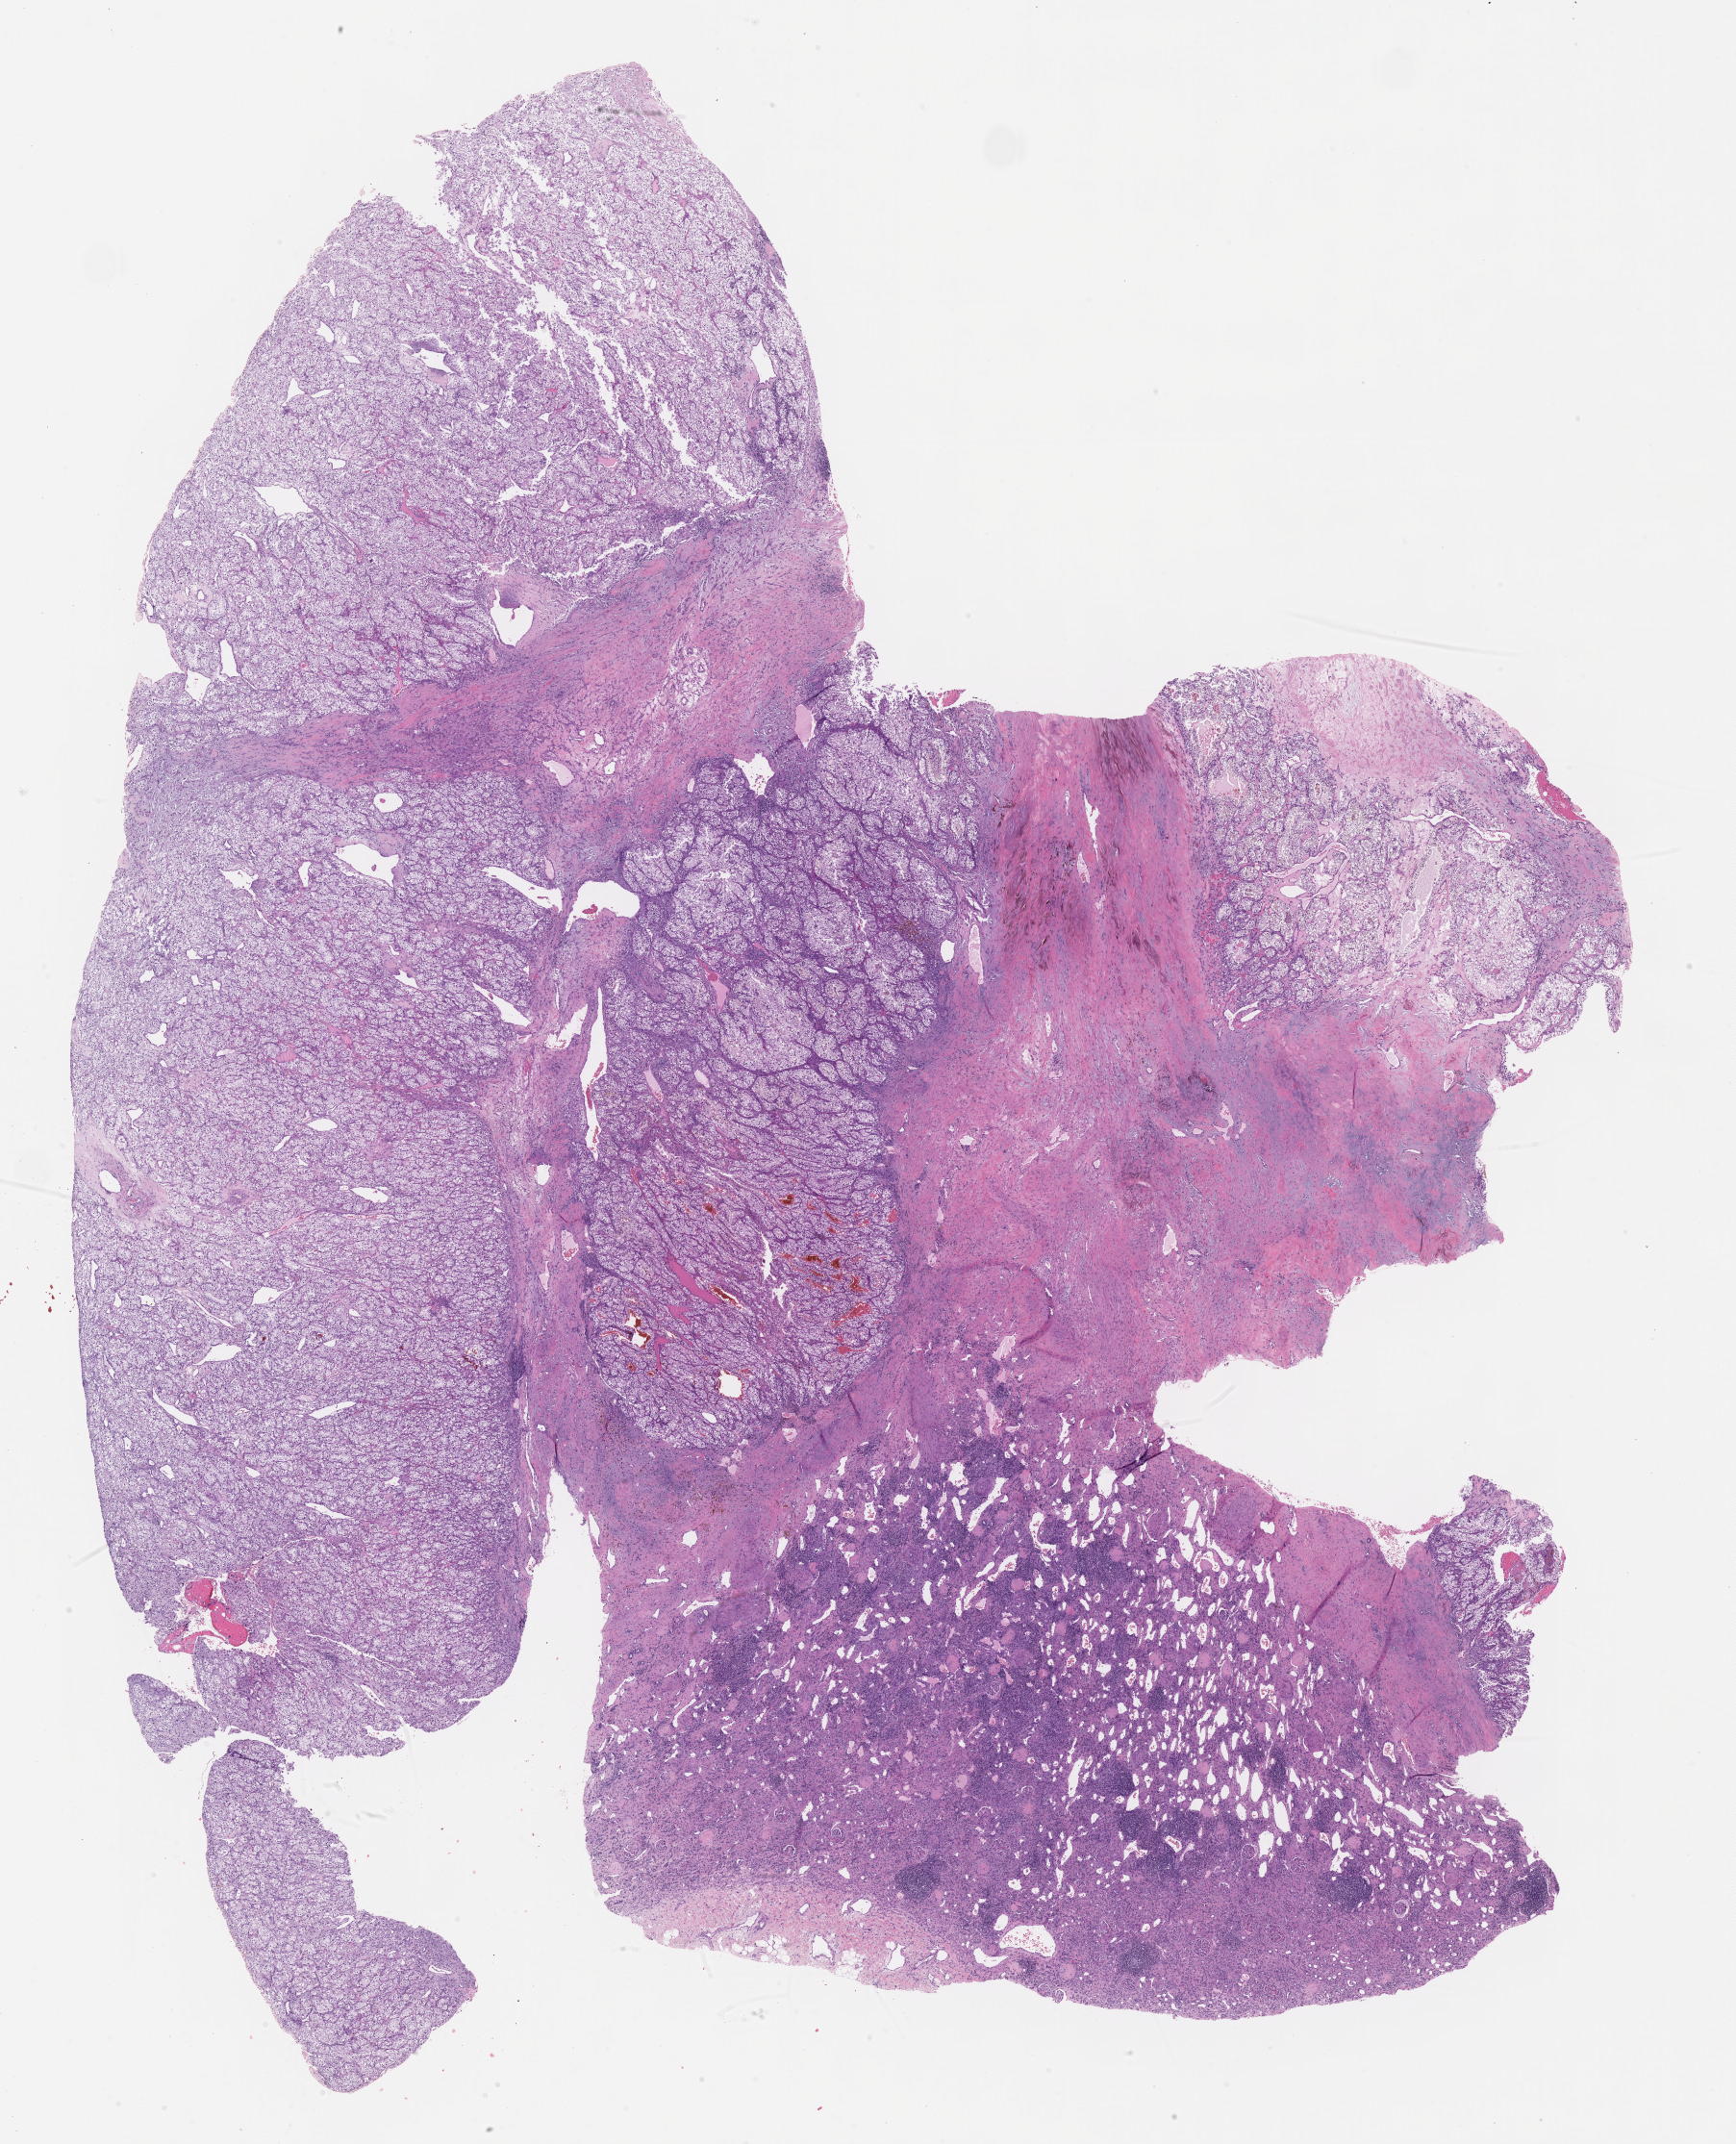
H&E-stained whole-slide image — low-resolution overview of the scanned area, about 14.6 x 18.0 mm (from a 40x scan). Formalin-fixed paraffin-embedded (FFPE) diagnostic section. Kidney, primary tumour sample. Male, age 61 years at initial diagnosis. Histologic grade: G3 (poorly differentiated).
TNM: T3a NX M0. Laterality: right. AJCC pathologic stage: III. Histologic diagnosis: Clear cell adenocarcinoma, NOS.